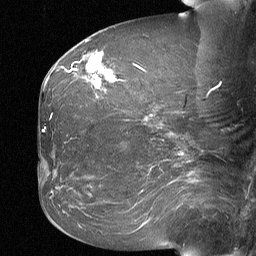
Breast MRI (dynamic contrast-enhanced), one sagittal slice. Position 27 of 64 along the scan axis. Dynamic contrast-enhanced study with each time point stored as its own series, time point 2 of 3 at this slice position (early post-contrast, ordered by acquisition time). 1.5 T. TE 4.8 ms, TR 27 ms. 2 mm slice thickness. 256 × 256 image matrix. Female patient, age 60 years. Case-level facts recorded for this patient, not image findings: setting: breast cancer imaged before/during neoadjuvant chemotherapy; receptor status: HR-positive, HER2-negative.
Structures marked on this image (semi-automatic segmentation, software-assisted and operator-edited):
- analysis volume of interest (the breast-tissue region the enhancement analysis was run in; not a lesion): bounding box [x1, y1, x2, y2] px = [80, 52, 114, 98]
- tumour enhancement mask (voxels above the 90 % enhancement threshold inside the analysis volume of interest): [89, 55, 112, 87]